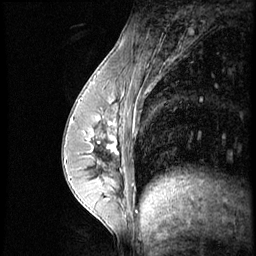
Breast MRI (dynamic contrast-enhanced), one sagittal slice. Slice 22 of 56 in the series (ordered by position). Dynamic contrast-enhanced series, image 2 of 4 at this slice position (ordered by acquisition). 1.5 T. TE 4.2 ms, TR 8.9 ms. 2.5 mm slice thickness. 256 × 256 image matrix, field of view 200 × 200 mm. Patient: female, 35 years. Case-level facts recorded for this patient, not image findings: setting: breast cancer imaged before/during neoadjuvant chemotherapy; receptor status: HER2-positive.
Outlined on this slice (semi-automatically segmented with operator editing):
- analysis volume of interest (the breast-tissue region the enhancement analysis was run in; not a lesion): bounding box <73,111,131,164> (left, top, right, bottom; pixels)
- tumour enhancement mask (voxels above the 140 % enhancement threshold inside the analysis volume of interest): <86,111,119,154>